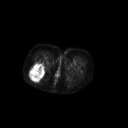
FDG PET of an extremity soft-tissue mass (from a PET/CT study), one axial slice. Position 49 of 267 along the scan axis. 3.27 mm slice thickness. 128 × 128 image matrix, field of view 700 × 700 mm. Female patient, age 70 years. Case-level facts recorded for this patient, not image findings: histological type: synovial sarcoma; grade: intermediate; site of the primary tumour: right buttock.
Outlined on this slice (expert contour drawn on MRI and transferred to this co-registered scan by the dataset authors):
- gross tumour volume including surrounding oedema: bounding box (x1, y1, x2, y2) in pixels: (29, 63, 45, 81)
- gross tumour volume (mass): (29, 63, 45, 81)